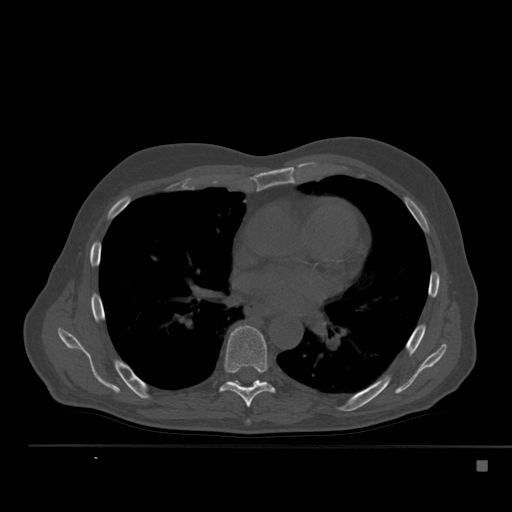
CT including the spine, one axial slice. Position 326 of 517 along the scan axis. 120 kVp. Bone window (W 1800 / L 400 HU). 1.5 mm slice thickness. 512 × 512 image matrix, field of view 408 × 408 mm. Male patient, age 70 years. From the clinical record (not read from this slice): primary cancer: renal.
Annotated regions visible in this slice (semi-automatic segmentation, software-assisted and operator-edited):
- T7 vertebra: bounding box <220,325,275,408> (left, top, right, bottom; pixels)